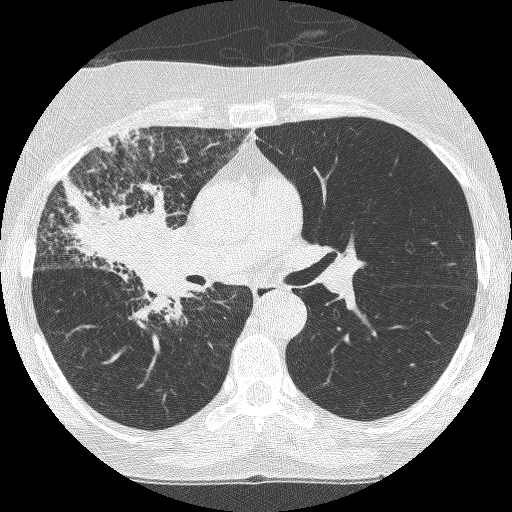
Axial slice from a low-dose chest CT screening exam, third screening round (two years after baseline), lung window (W 1500 / L -600 HU), 1.25 mm slice thickness, 120 kVp. Female, age 64 years at enrolment. Former smoker at enrolment.
Expert reader's lesion annotation, bounding box <69,185,202,320> (left, top, right, bottom; pixels). Reader record for this screening exam (exam-level; its link to the box is not recorded): non-calcified nodule or mass ≥4 mm, right upper lobe, 49 × 43 mm, spiculated (stellate) margins, soft tissue attenuation, pre-existing on the prior screen: yes; interval growth: yes. Official screen result: positive, other.